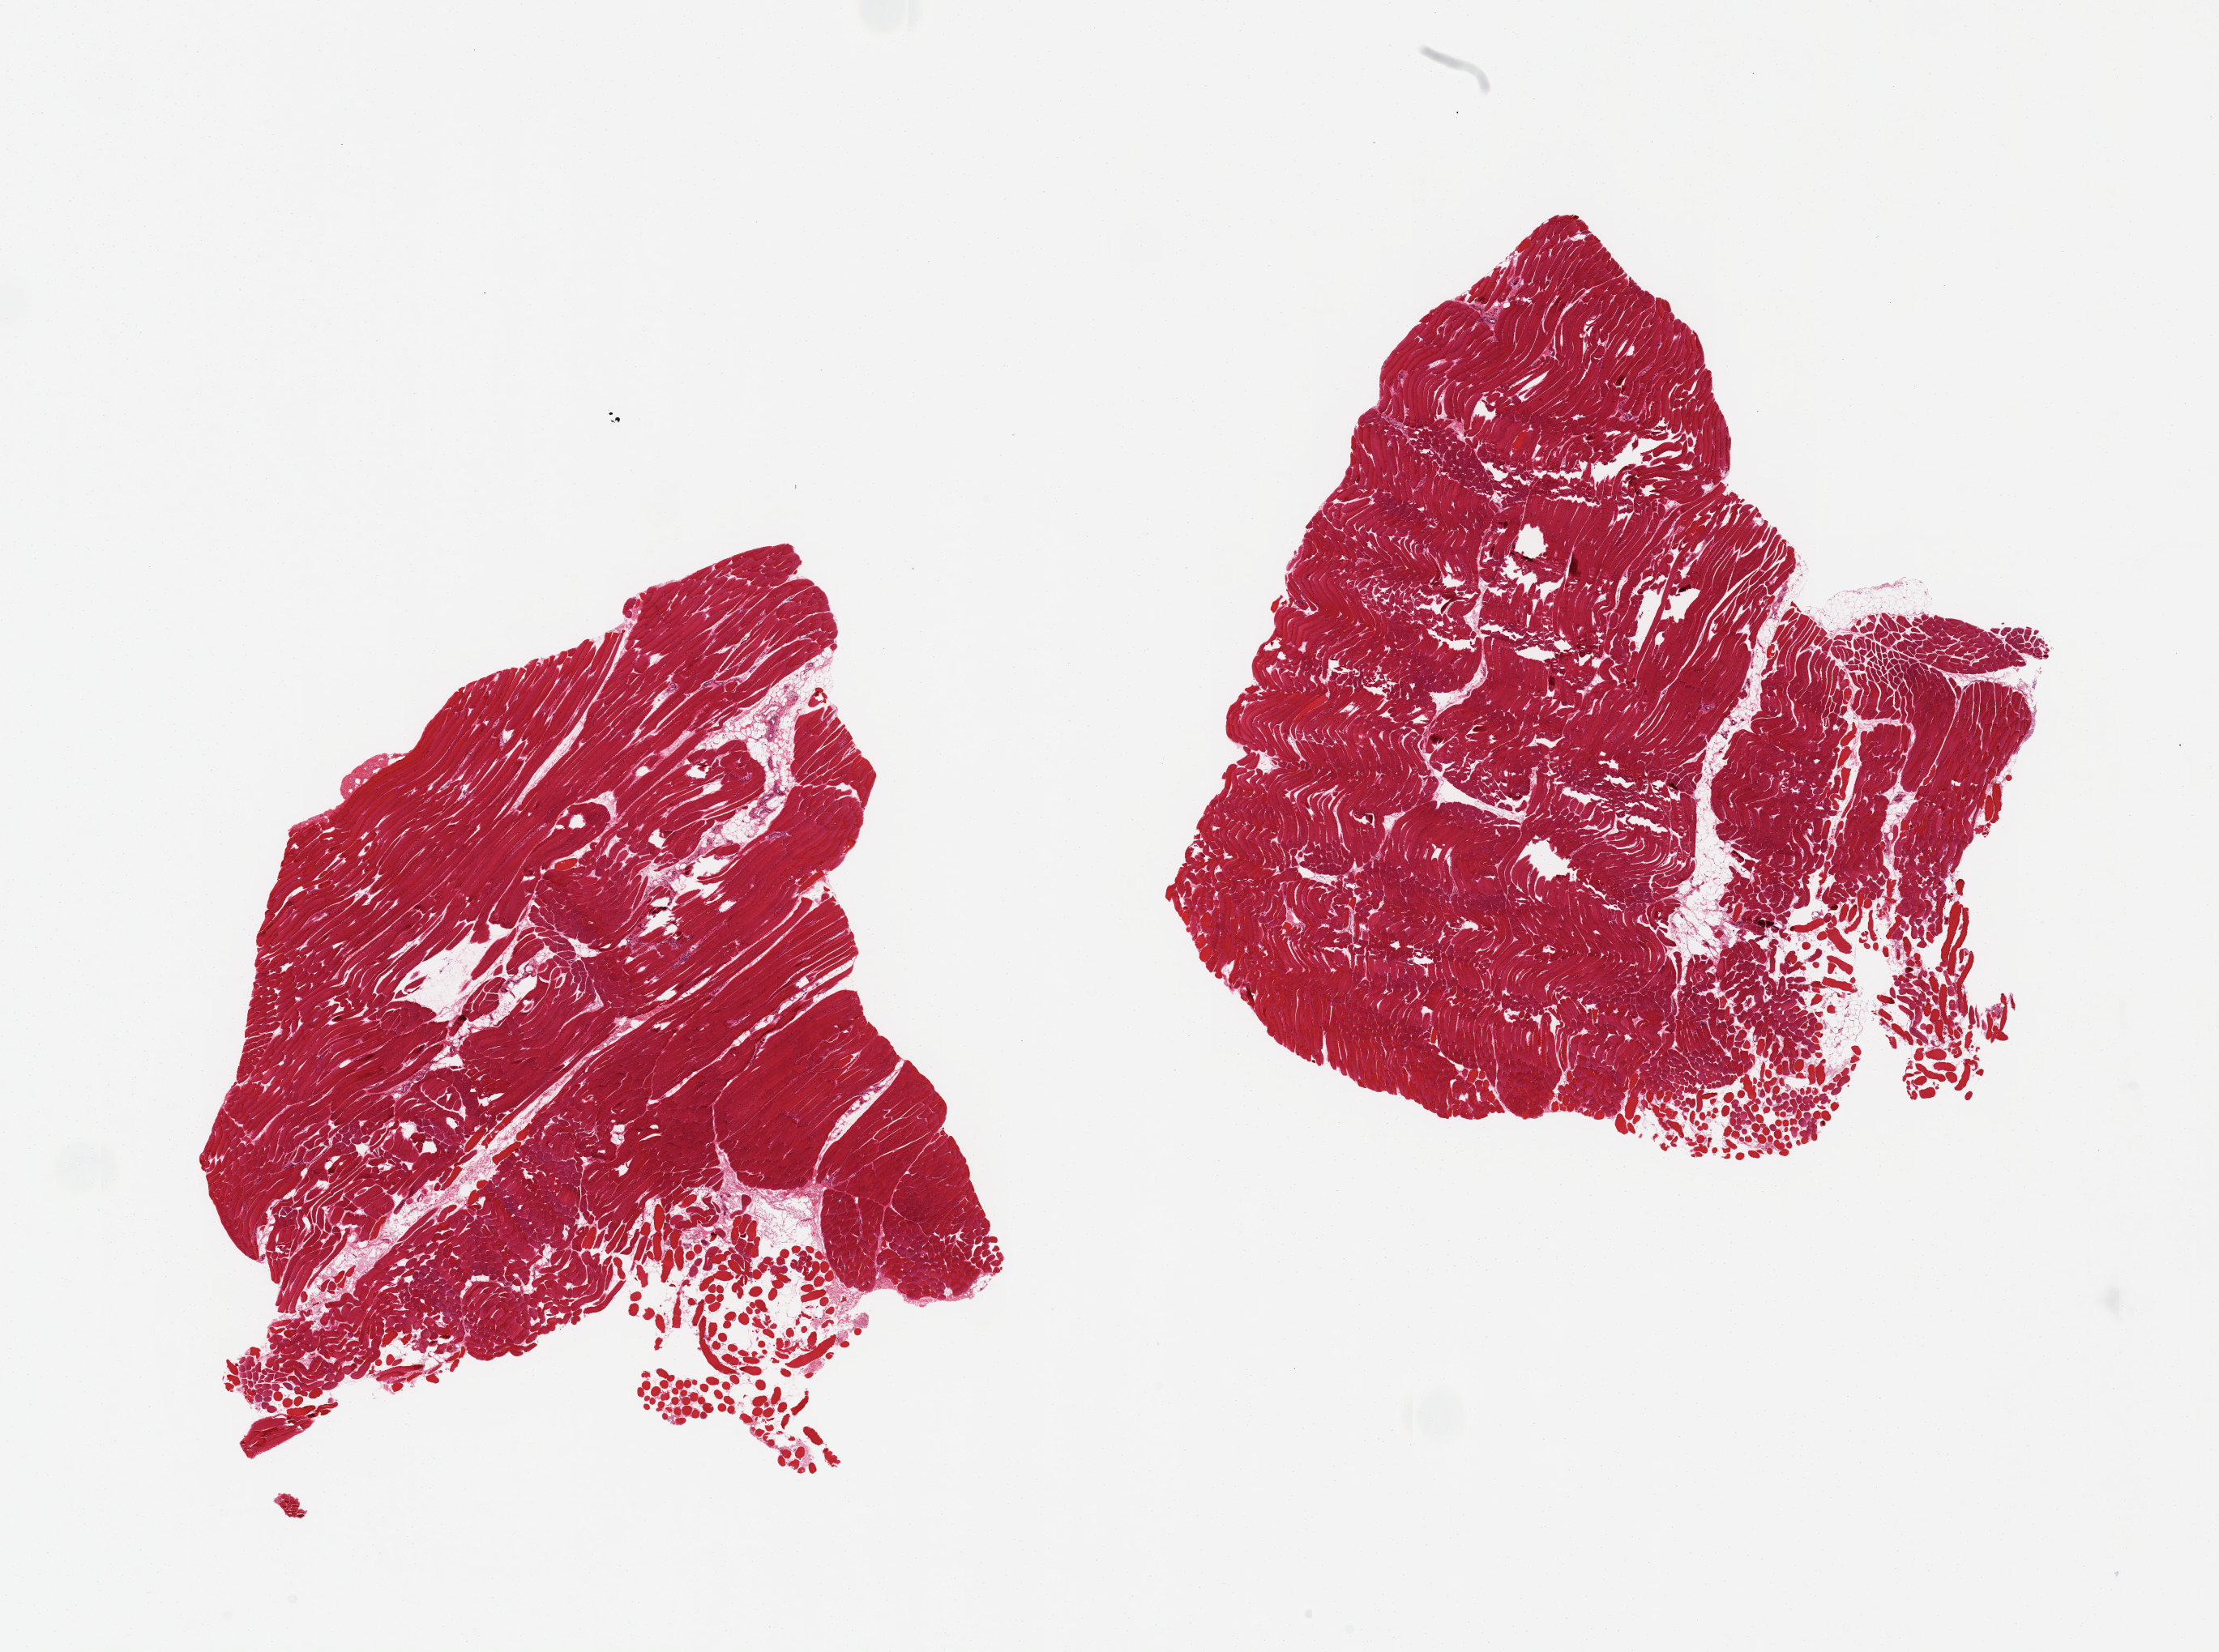
Haematoxylin and eosin whole-slide image — low-resolution overview of the scanned area, about 21.7 x 16.1 mm (acquisition: 20x scan), PAXgene-fixed, paraffin-embedded tissue, section of skeletal muscle (target tissue), donor tissue sample. Male donor.
Review note (as recorded): 2 pieces ~8x7mm, minimal interstitial fat.